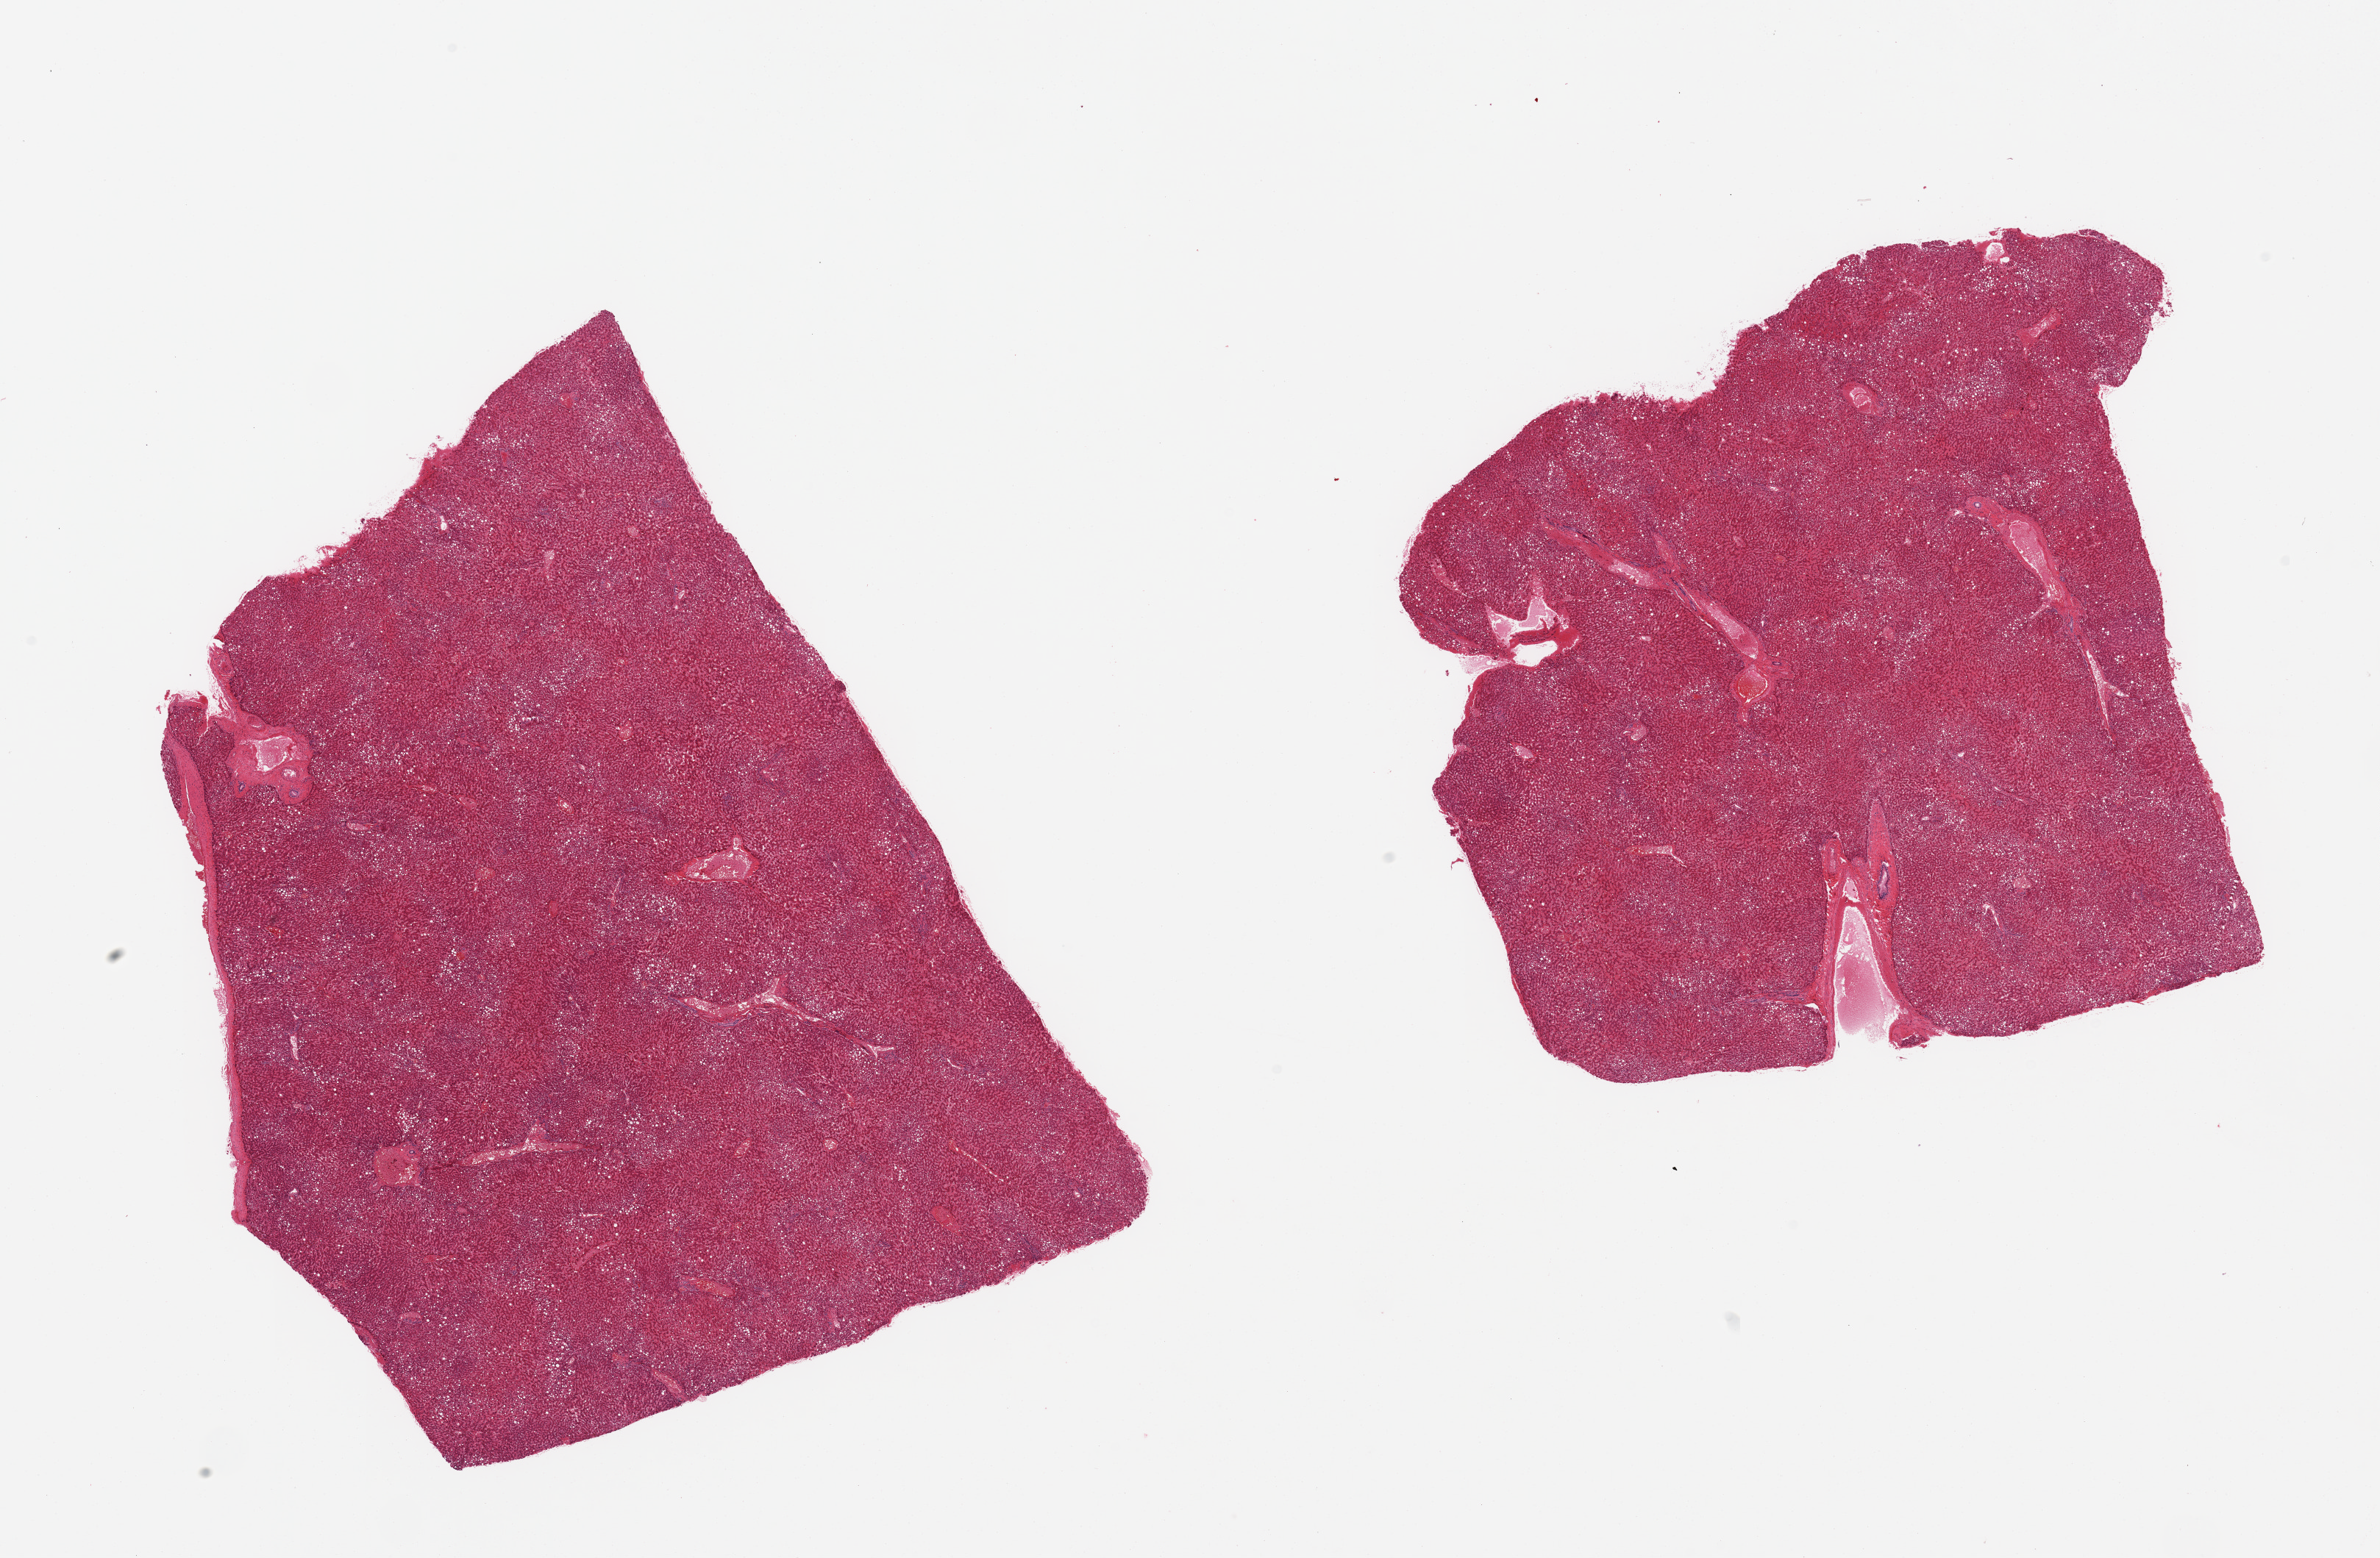
Digitized hematoxylin and eosin (H&E)-stained section, low-resolution overview of the scanned area, about 25.6 x 16.8 mm (acquisition: 20x scan); PAXgene-fixed paraffin-embedded (PFPE) section; target tissue: liver; tissue donor sample. Male donor.
Pathologist's review note for this sample: 2 pieces; congestion, mild steatosis.